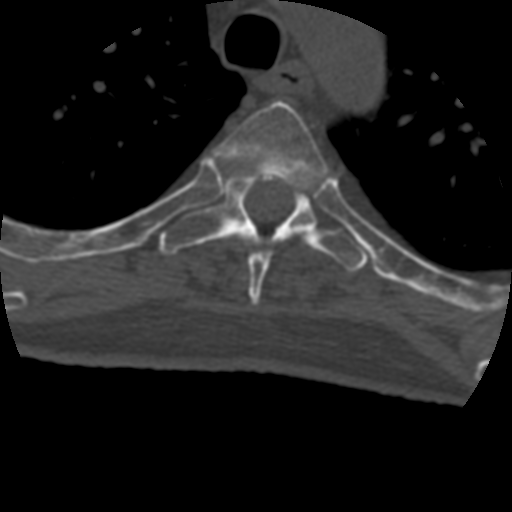
CT including the spine, one axial slice; slice 327 of 399 in the series (ordered by position); reconstruction kernel STANDARD; bone window (W 1800 / L 400 HU); 1.25 mm slice thickness; 512 × 512 image matrix. Patient age 69 years. Case-level facts recorded for this patient, not image findings: primary cancer: prostate.
Outlined on this slice (semi-automatic segmentation, software-assisted and operator-edited):
- T4 vertebra: bounding box <215,101,328,306> (left, top, right, bottom; pixels)
- T5 vertebra: <159,172,368,272>